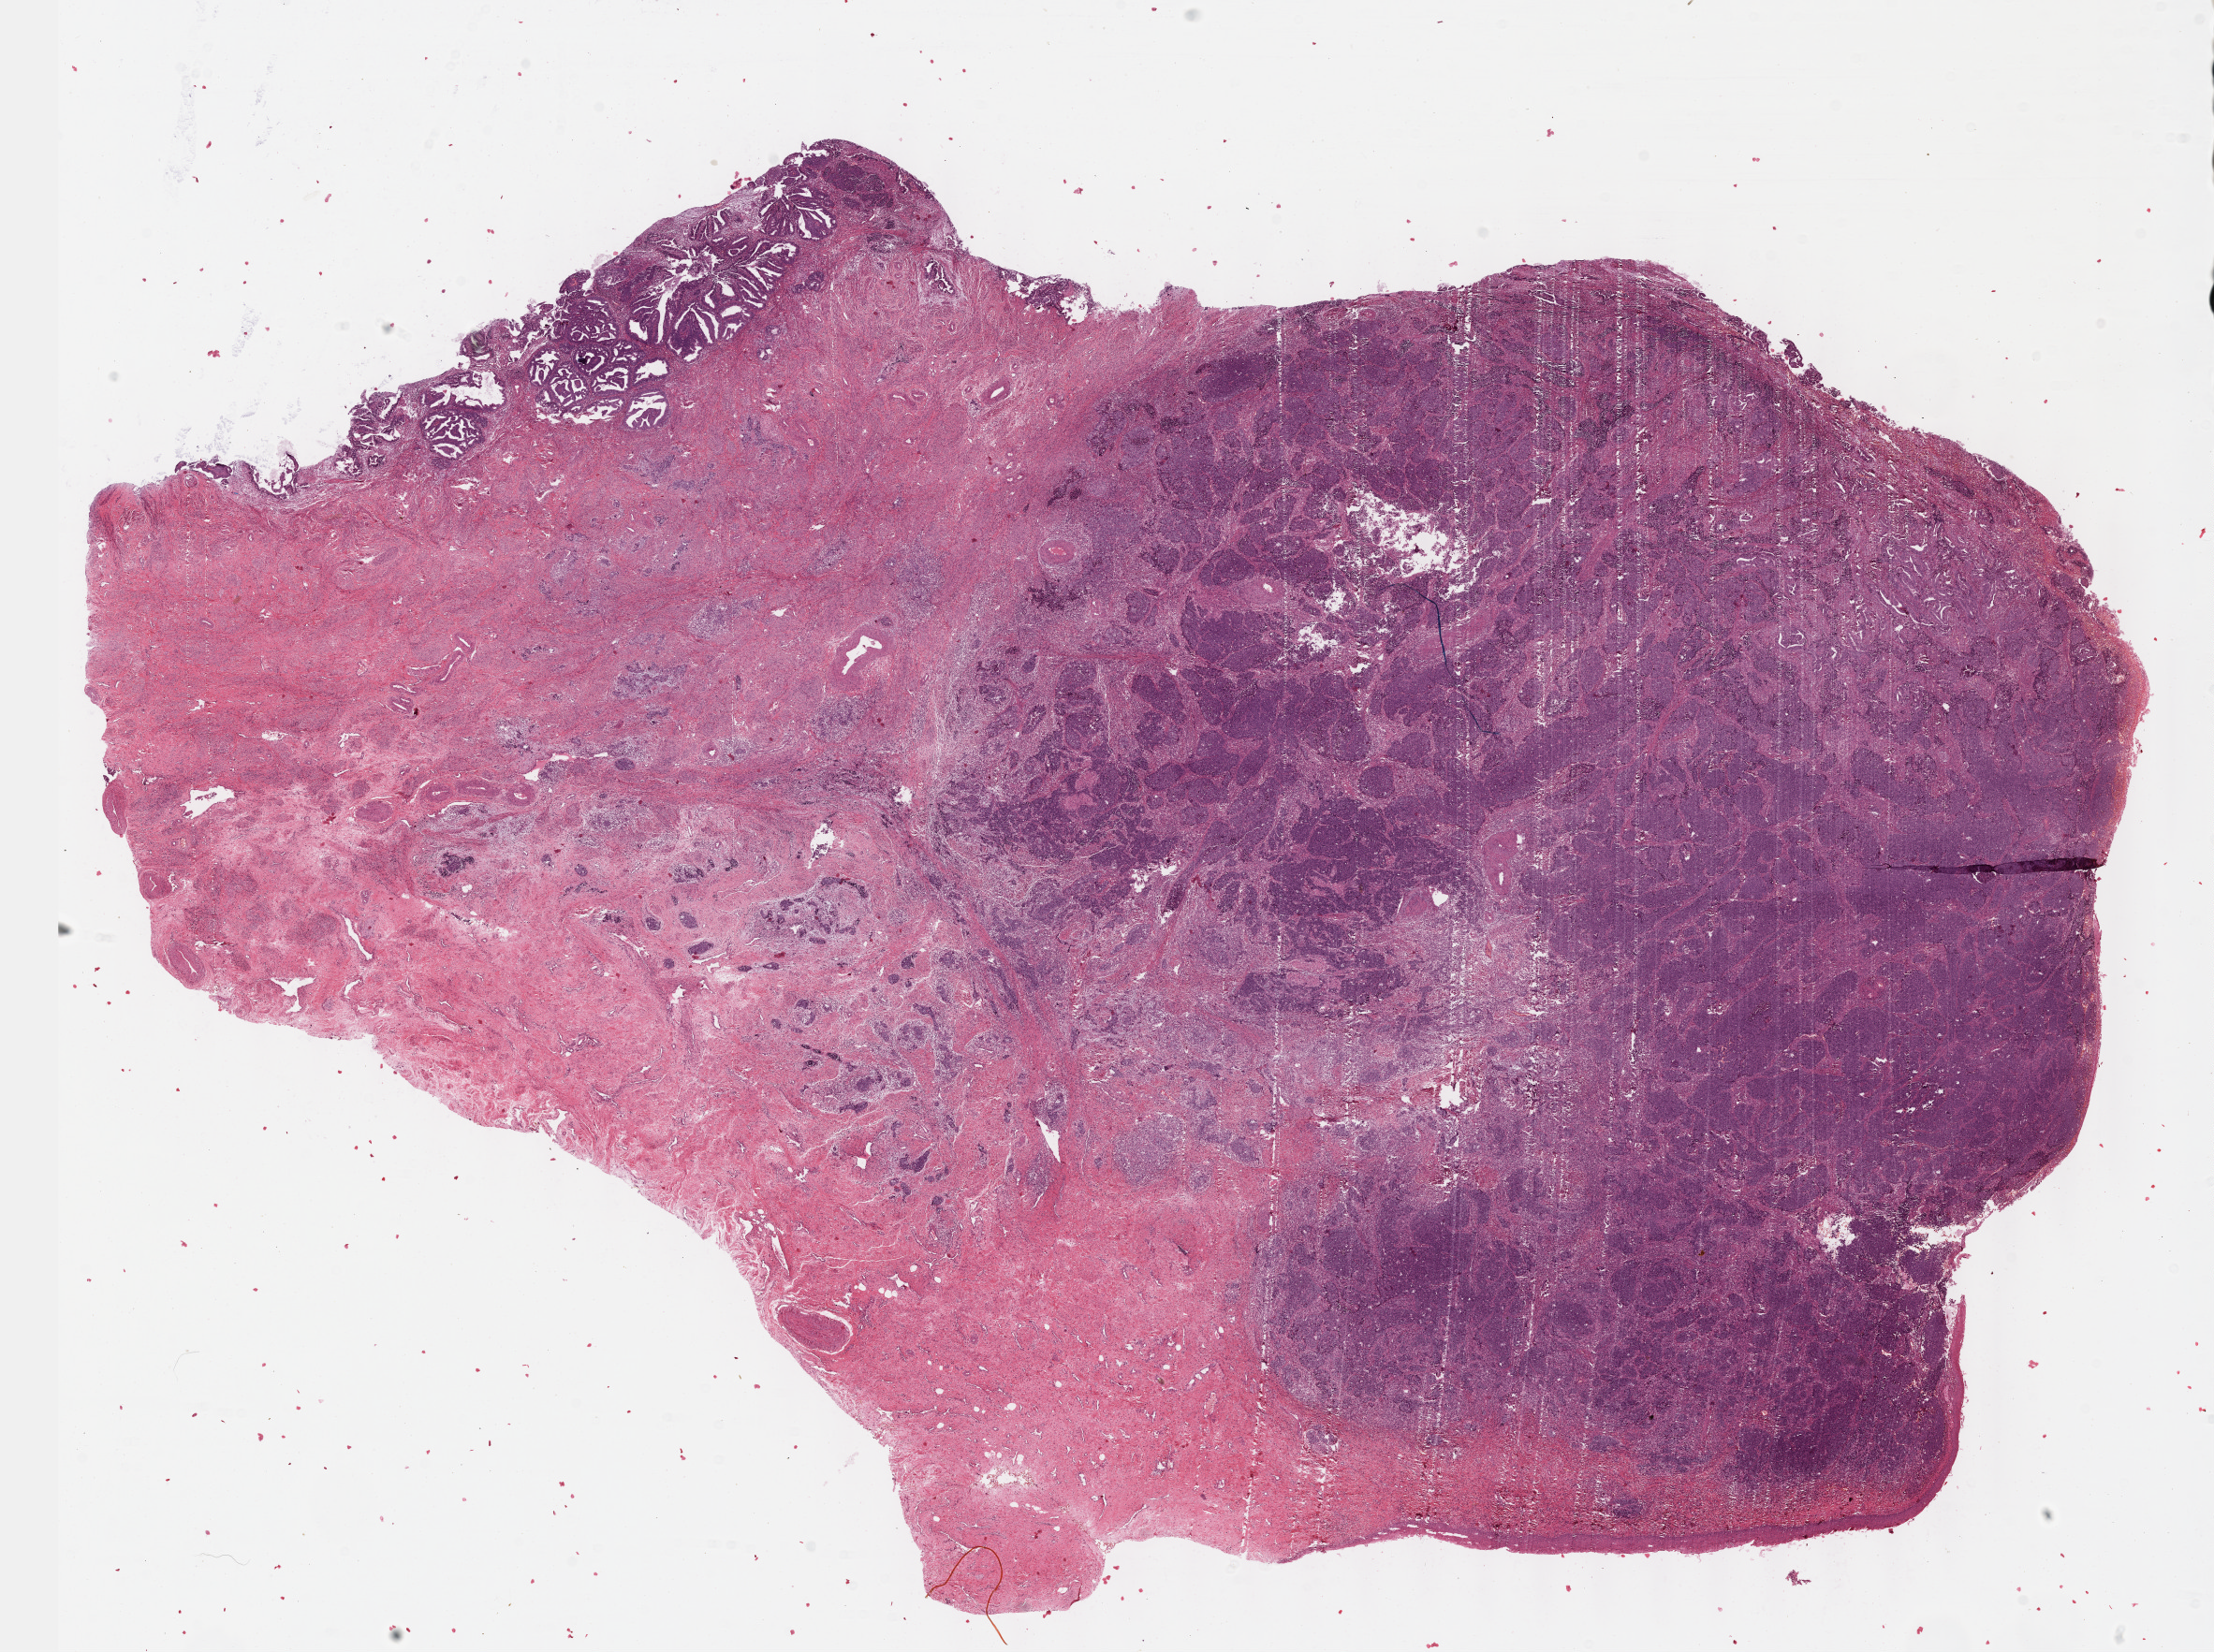
Whole-slide histology image, H&E — whole scanned area (about 19.1 x 14.3 mm, from a 40x scan) shown as a low-resolution overview; formalin-fixed paraffin-embedded (FFPE) diagnostic section; cervix, primary tumour sample. Female patient; age at initial diagnosis 53 years. Histologic grade: G3 (poorly differentiated).
- FIGO stage: II
- lymph nodes positive (case pathology): 0 of 2 examined
- histologic diagnosis: Adenocarcinoma, endocervical type (cervix uteri)